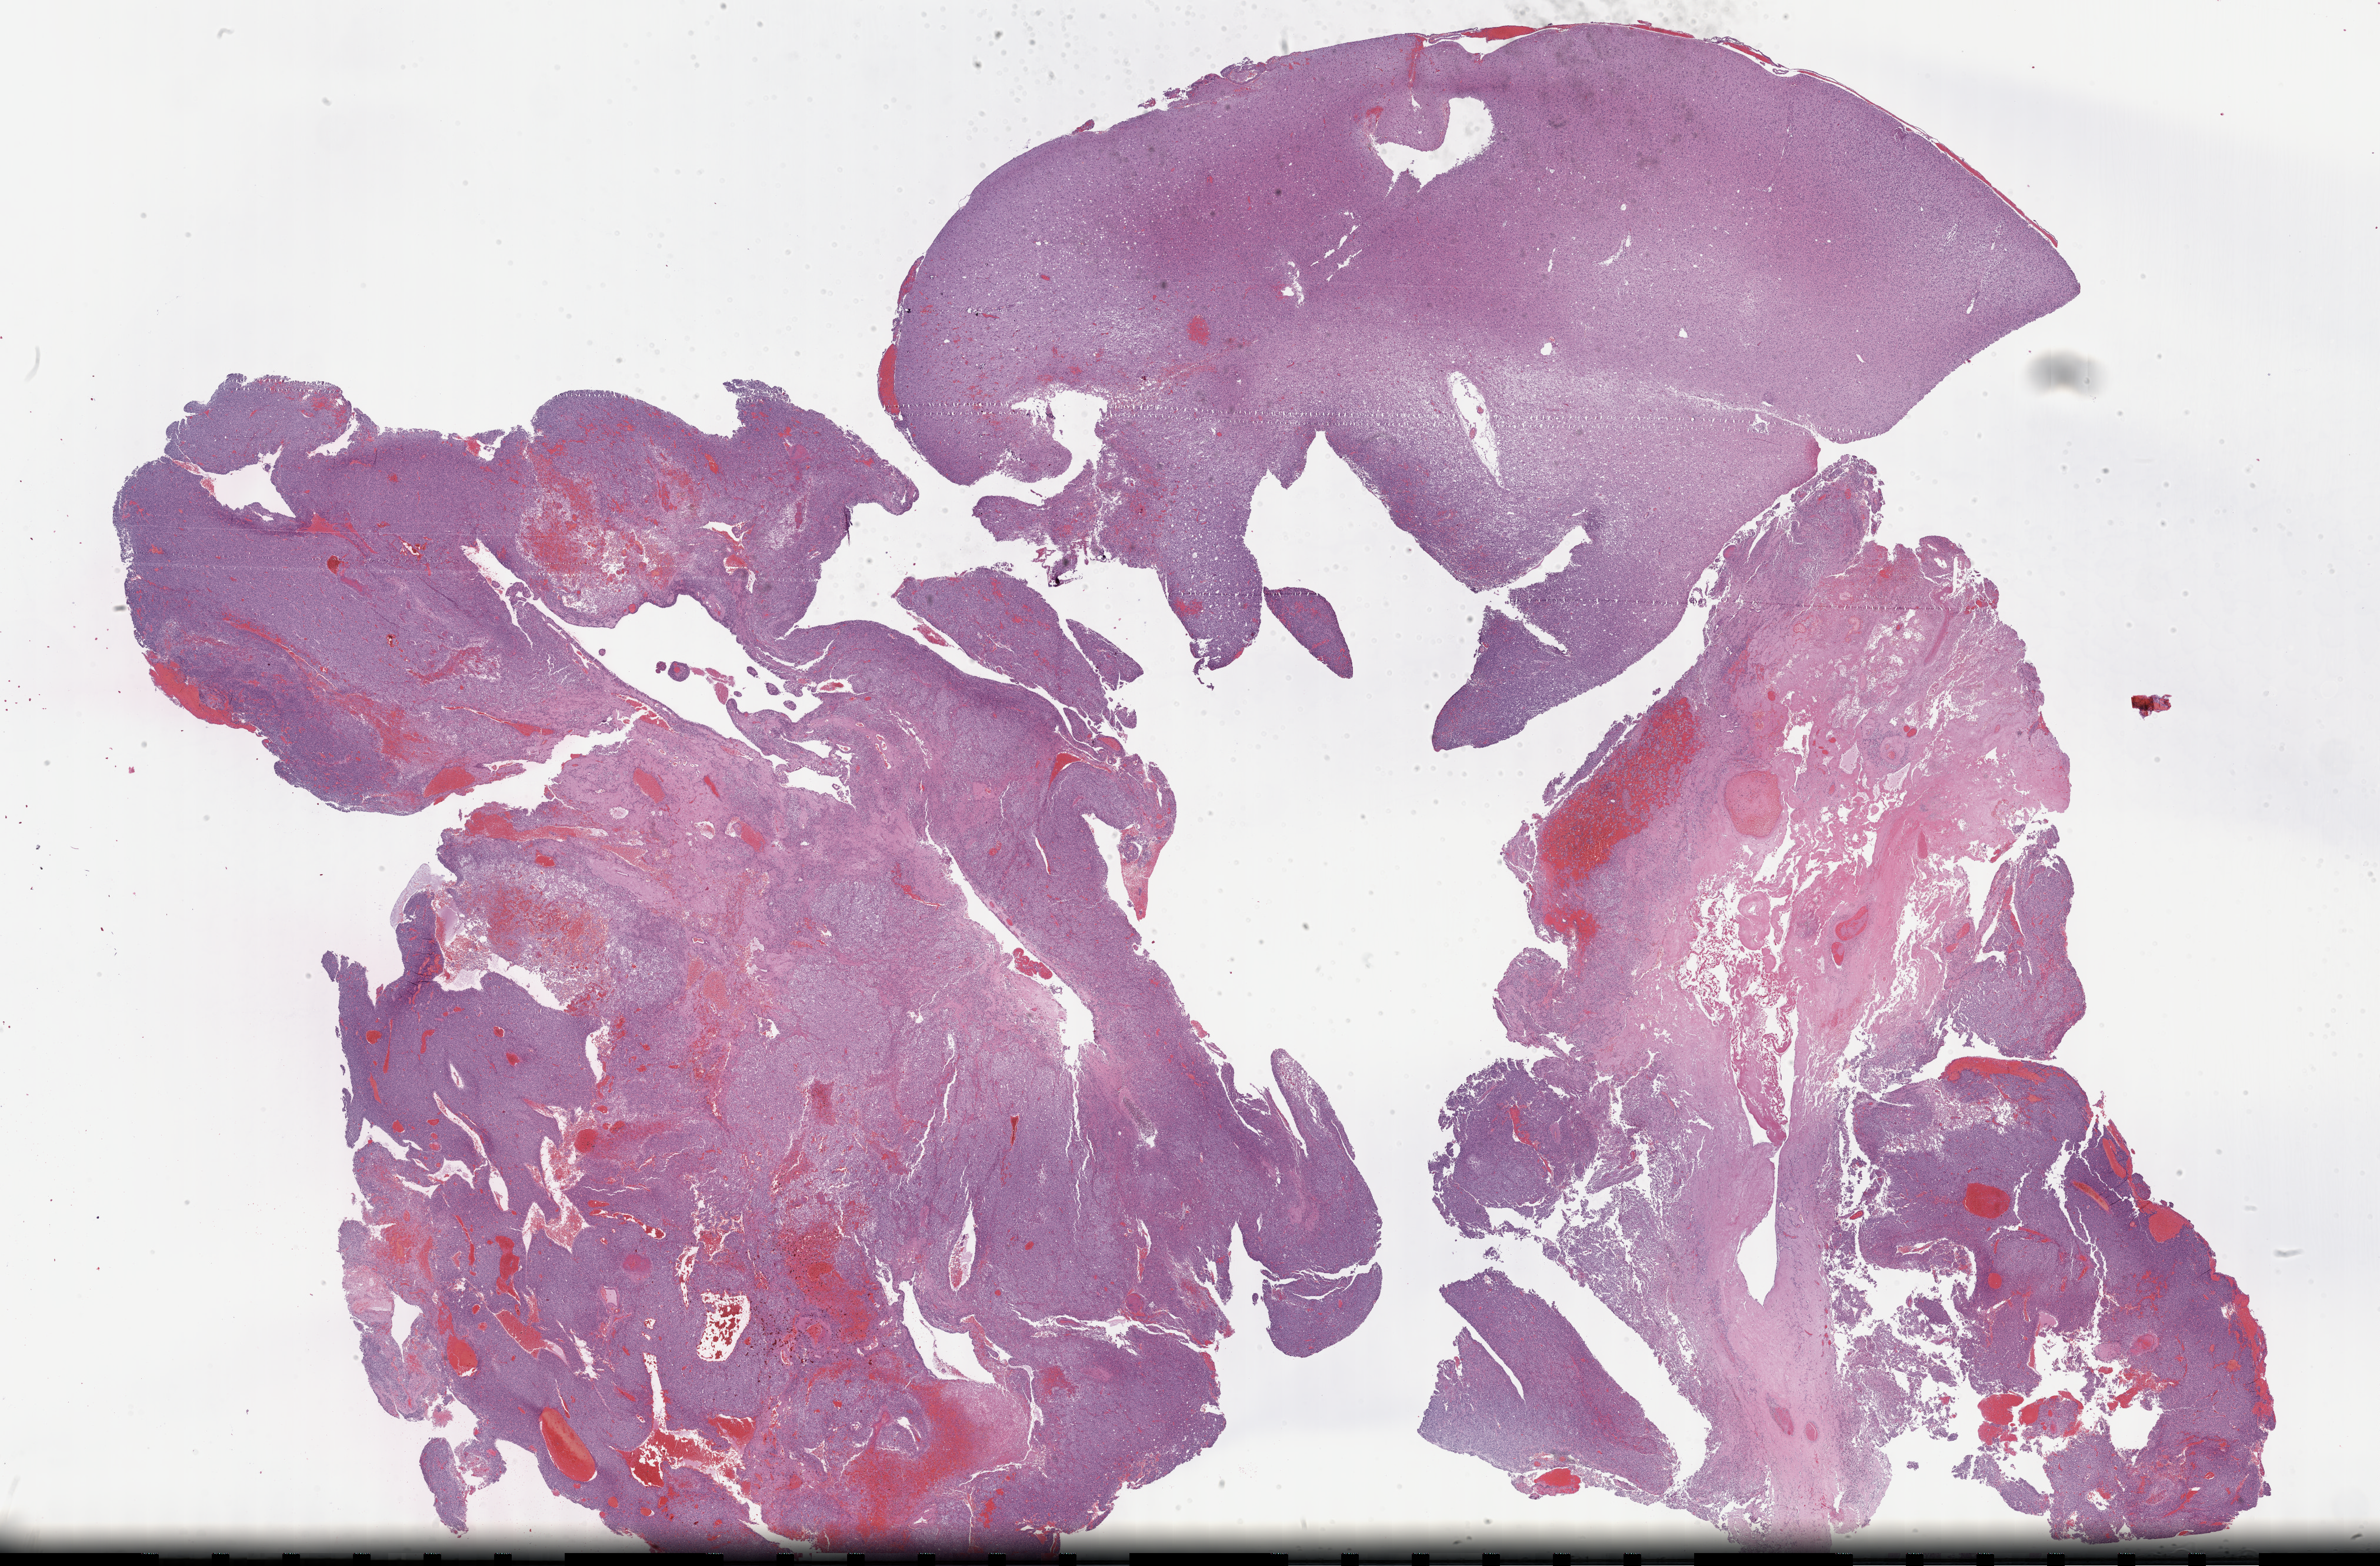
H&E whole-slide image, low-resolution overview of the scanned area, about 32.7 x 21.5 mm, FFPE section, brain, primary tumour sample. Male, age 33 years at initial diagnosis. Histologic grade: G3 (poorly differentiated).
• histologic diagnosis: Oligodendroglioma, anaplastic (cerebrum)